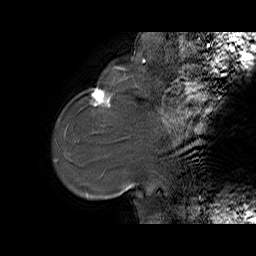
Breast MRI (dynamic contrast-enhanced), one sagittal slice. Dynamic contrast-enhanced series, time point 2 of 6 at this slice position (early post-contrast). 1.5 T. TE 5.7 ms, TR 32.9 ms. 4 mm slice thickness. 256 × 256 image matrix, field of view 230 × 230 mm. Female patient. From the clinical record (not read from this slice): setting: breast cancer imaged before/during neoadjuvant chemotherapy; receptor status: HER2-positive.
Annotated regions visible in this slice (semi-automatic segmentation, software-assisted and operator-edited):
- analysis volume of interest (the breast-tissue region the enhancement analysis was run in; not a lesion): bounding box [x1, y1, x2, y2] px = [78, 77, 125, 128]
- tumour enhancement mask (voxels above the 100 % enhancement threshold inside the analysis volume of interest): [92, 89, 111, 105]